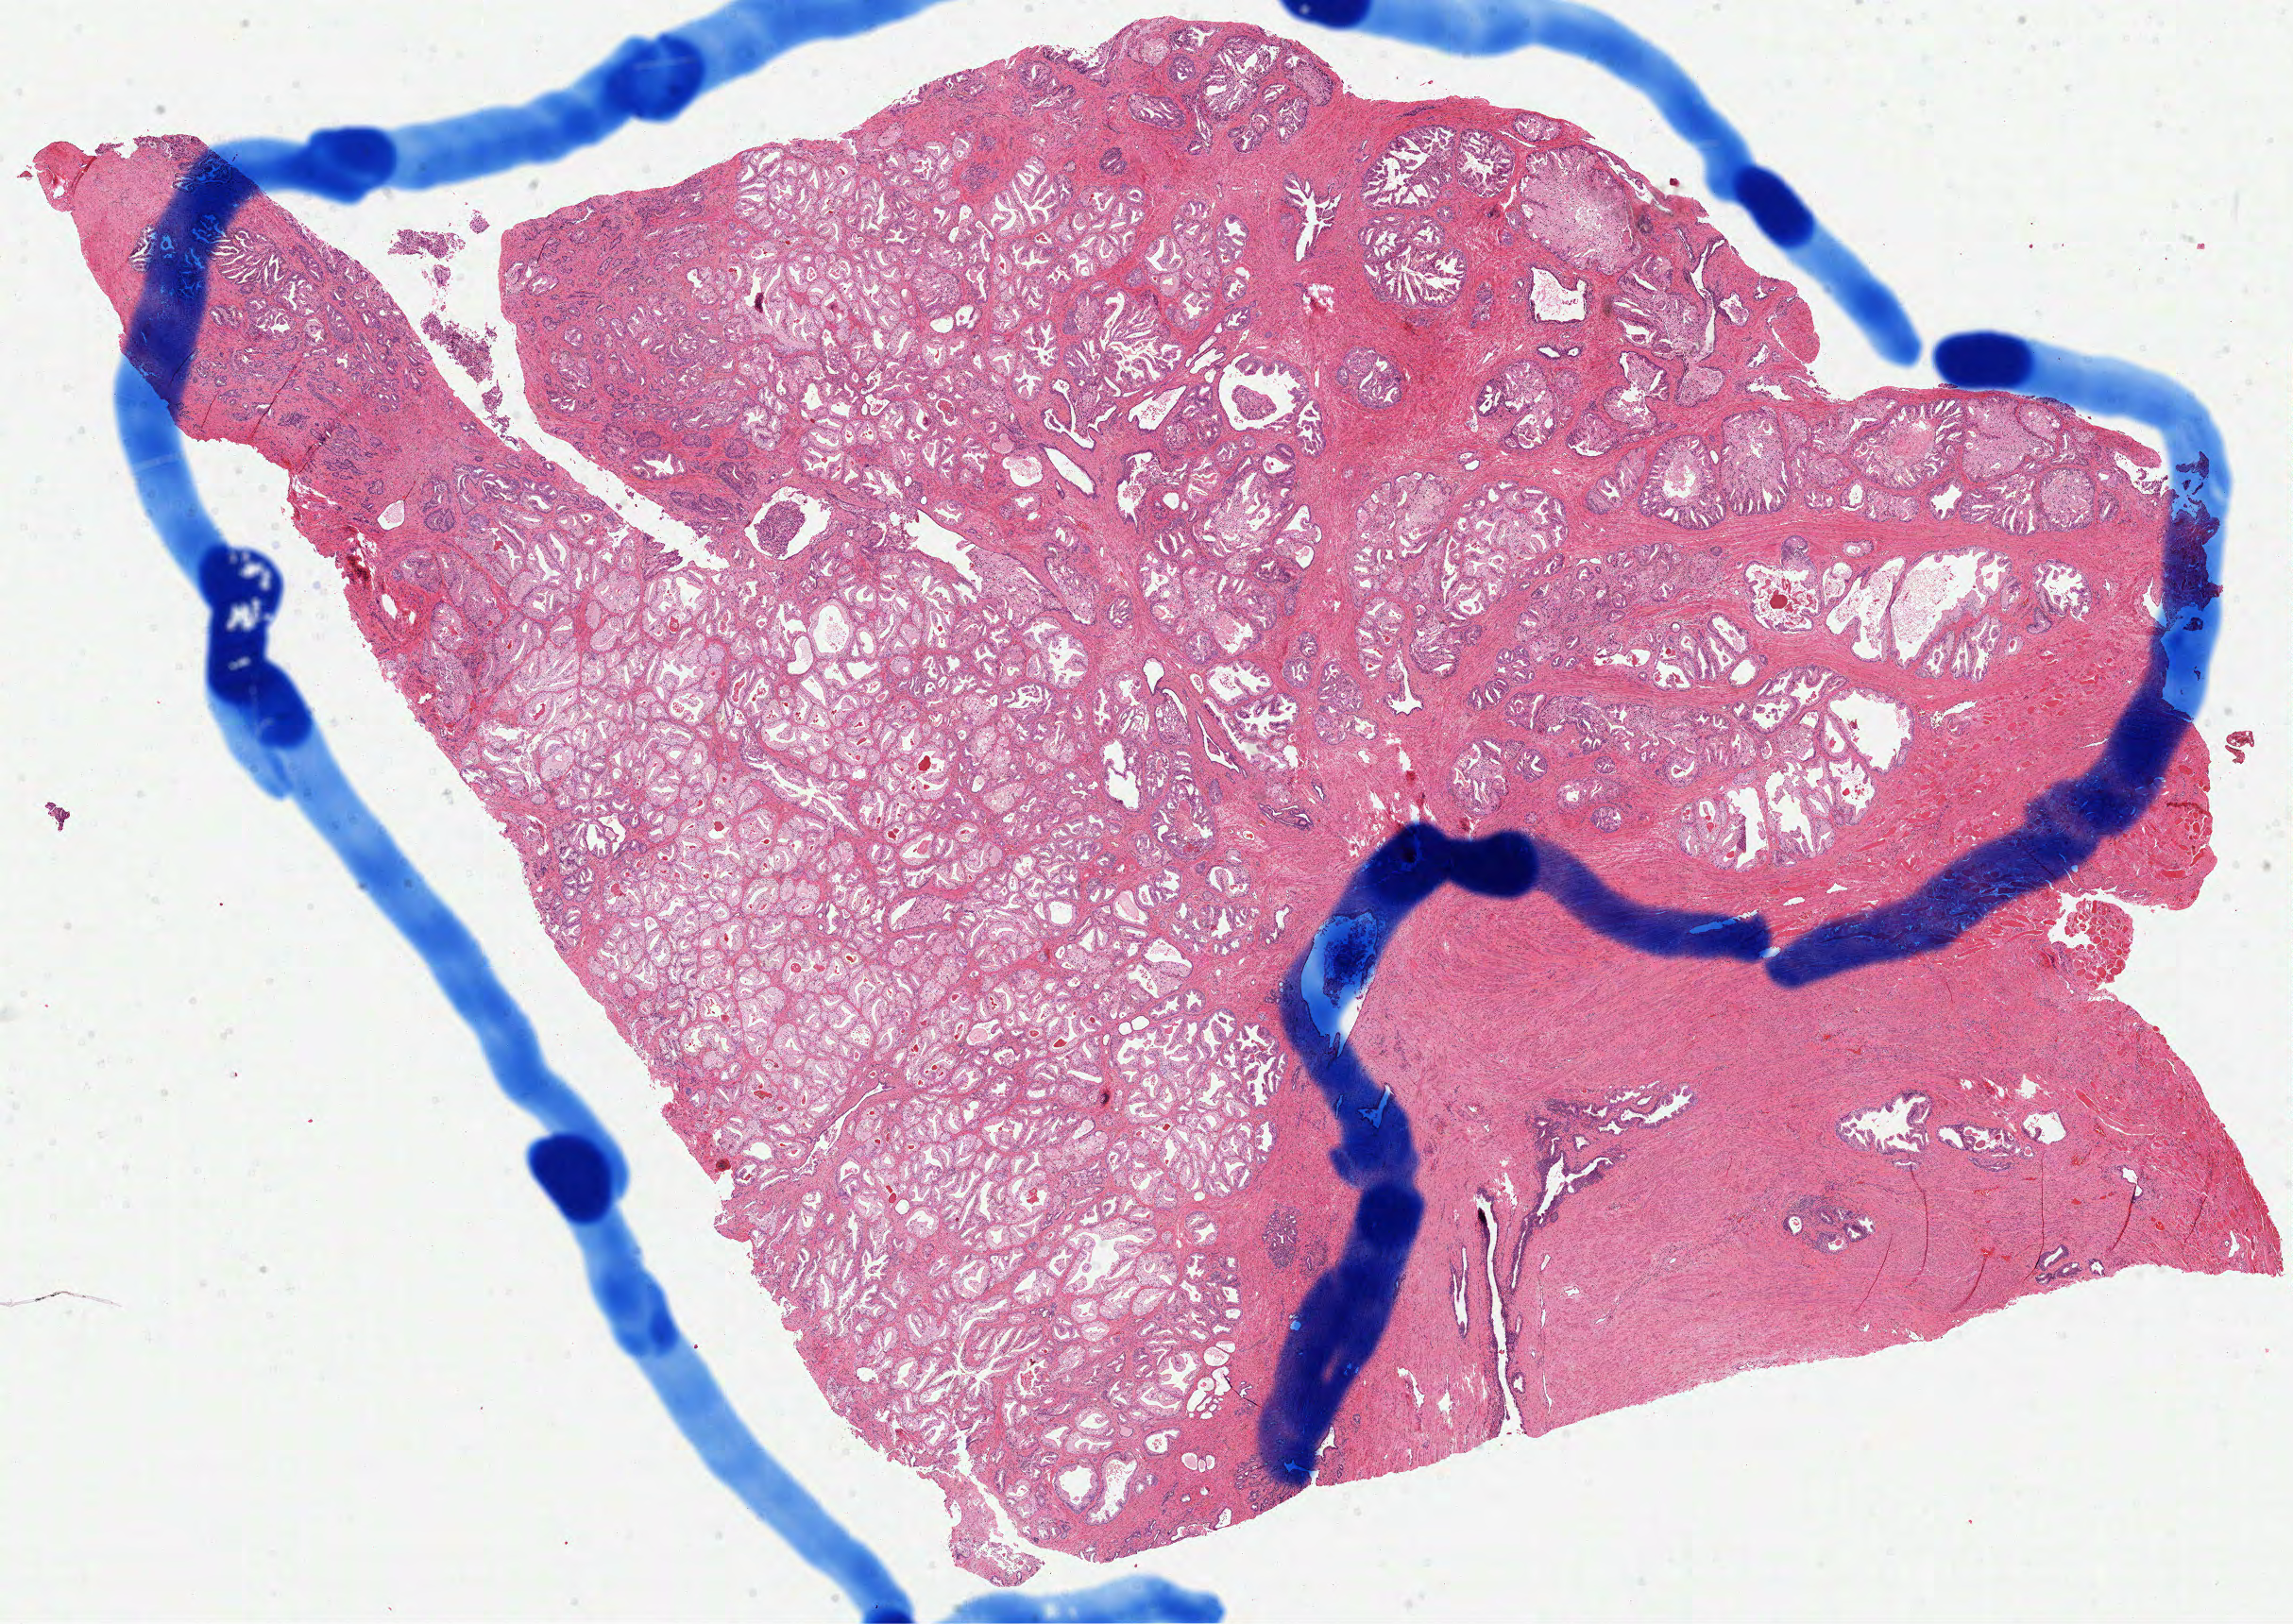
H&E-stained whole-slide image, shown as a low-resolution overview of the whole scanned area (about 19.6 x 13.9 mm); formalin-fixed paraffin-embedded (FFPE) diagnostic section; sample: primary tumour, prostate. Male, age 63 years at initial diagnosis. Gleason score: 7 (3+4).
* pathologic diagnosis: Acinar cell carcinoma (prostate gland)
* lymph nodes positive (case pathology): 0 of 2 examined
* laterality: right